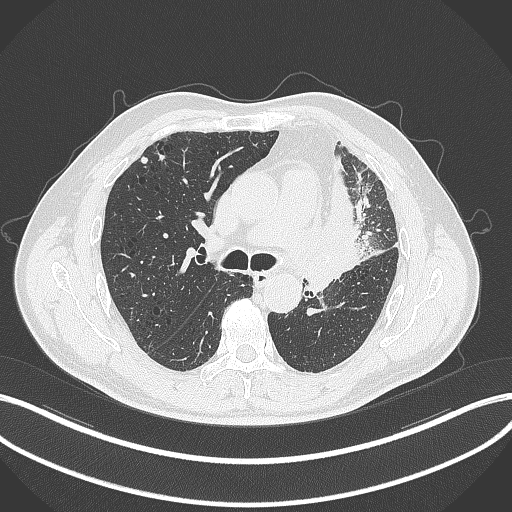
Chest CT, one axial slice. Position 188 of 297 along the scan axis. Reconstruction kernel B70f. Lung window (W 1500 / L -600 HU). 1 mm slice thickness. 512 × 512 image matrix, field of view 400 × 400 mm. Patient: male, 68 years. Case-level facts recorded for this patient, not image findings: clinical TNM (as recorded): T3 N3 M1.
Outlined on this slice (bounding box drawn by a radiologist):
- lung tumour (recorded histology: adenocarcinoma): bounding box (x1, y1, x2, y2) in pixels: (326, 163, 378, 271)